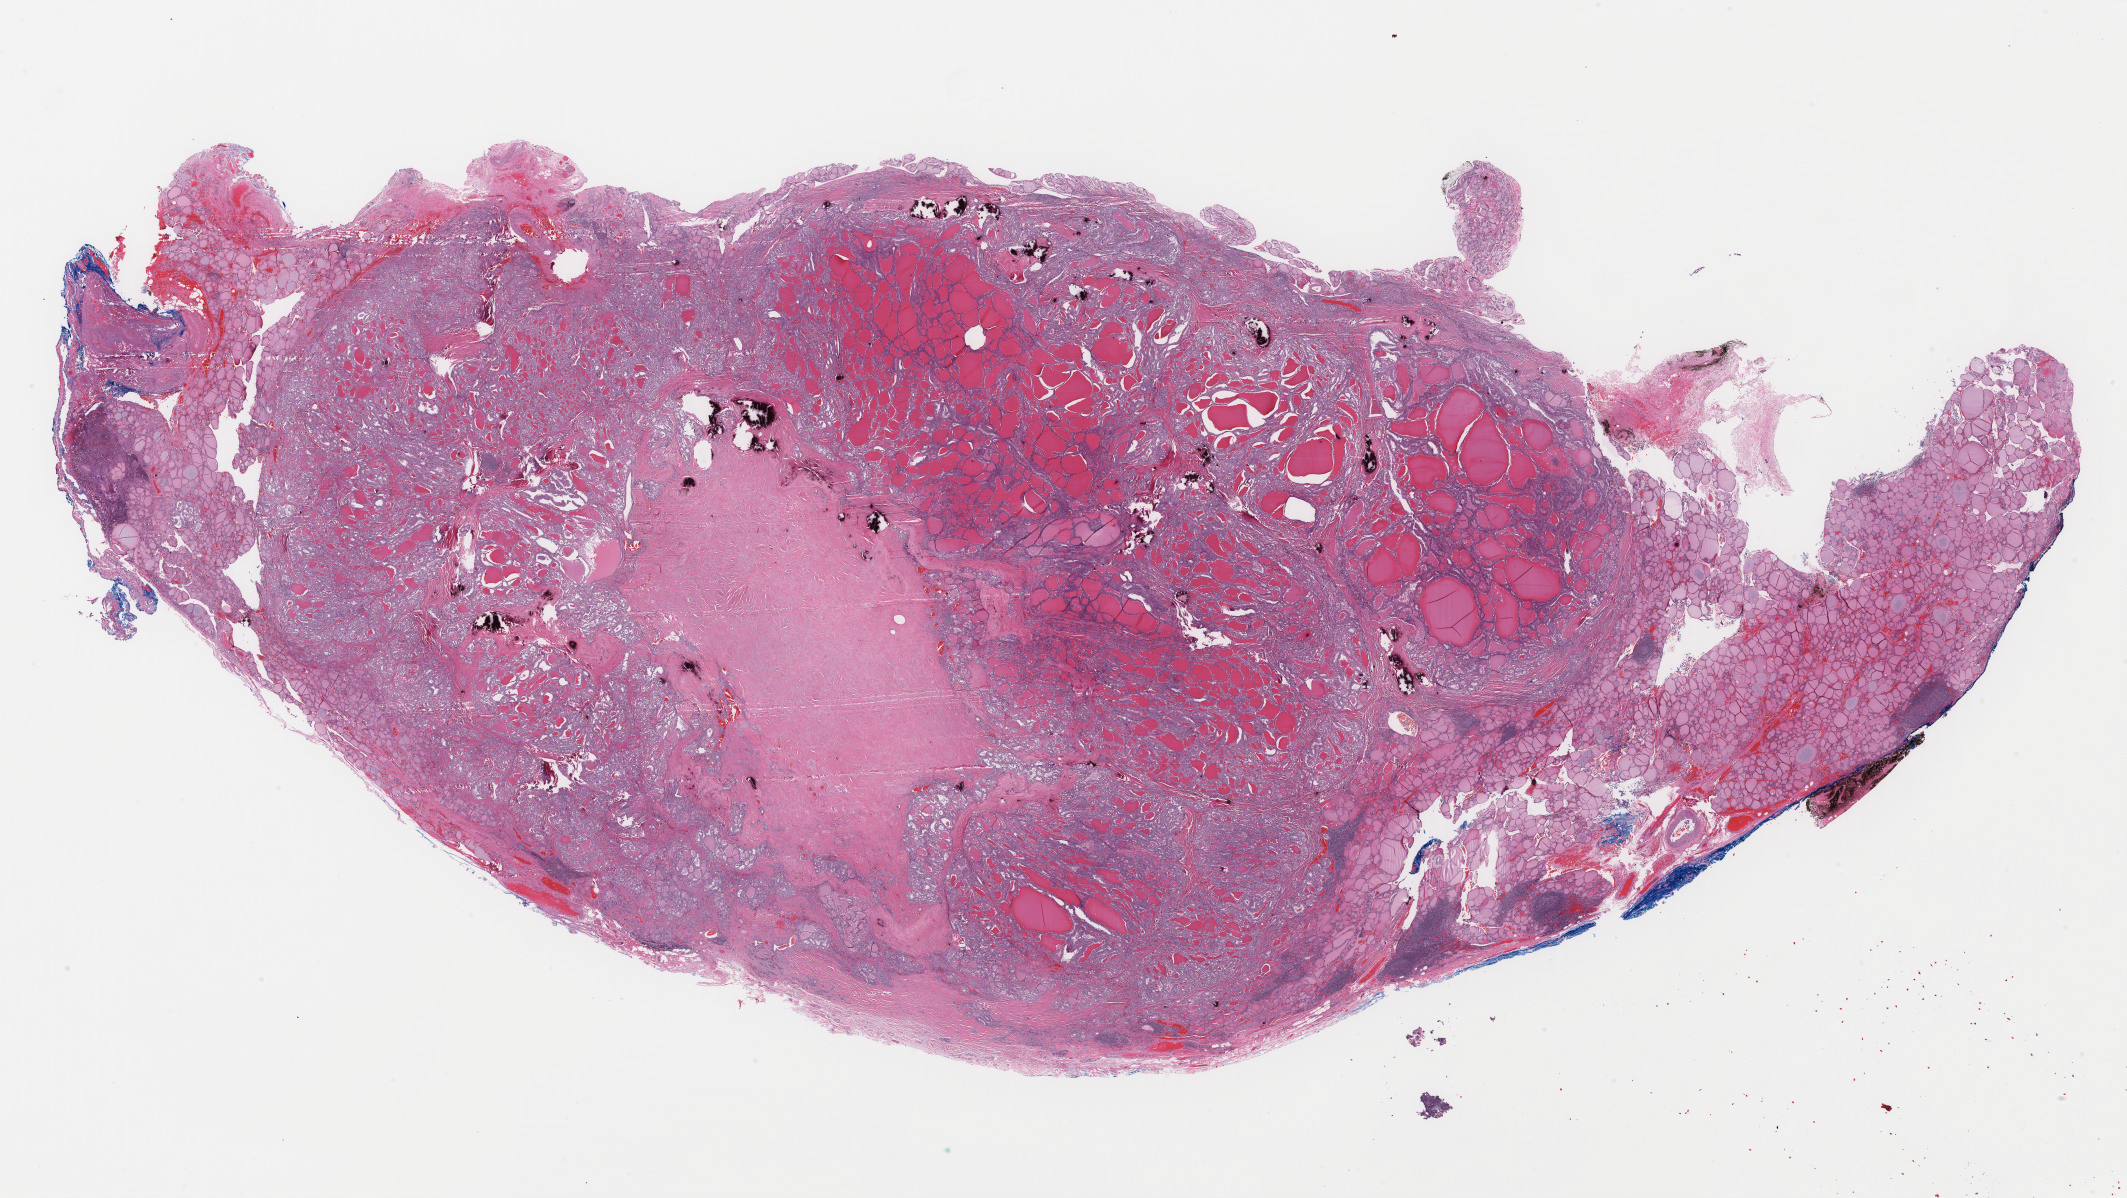
Whole-slide histology image, H&E-stained, whole scanned area (about 33.8 x 19.0 mm, slide scanned at 40x) shown as a low-resolution overview, formalin-fixed paraffin-embedded (FFPE) diagnostic section, primary tumour sample from the thyroid. Female patient; age at initial diagnosis 52 years.
• AJCC pathologic stage: III (7th edition)
• laterality: bilateral
• pathologic diagnosis: Papillary adenocarcinoma, NOS (thyroid gland)